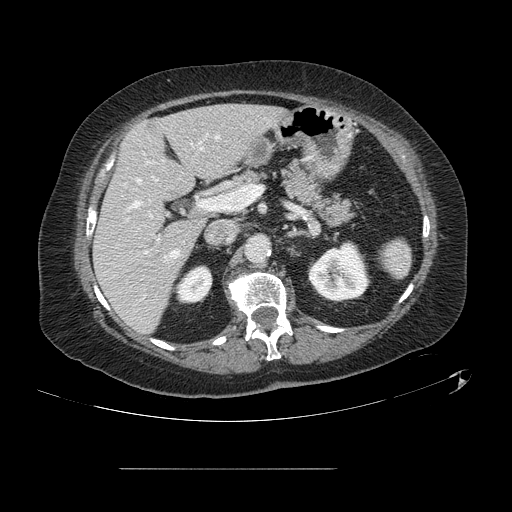
Contrast-enhanced abdominal CT, one axial slice. Position 67 of 148 along the scan axis. Intravenous contrast given. Soft-tissue window (W 400 / L 40 HU). 2.5 mm slice thickness. 512 × 512 image matrix, field of view 439 × 439 mm. Female patient, age 75 years. From the clinical record (not read from this slice): diagnosis: colorectal cancer liver metastases, imaged before liver resection; multiple liver metastases: no; largest metastasis: 2.4 cm; disease in both lobes: no.
Structures marked on this image (manually delineated by an expert):
- hepatic veins: box from (x=128, y=136) to (x=219, y=258) px
- liver: (x=94, y=105)–(x=284, y=333)
- planned liver remnant (the part of the liver to remain after resection): (x=95, y=105)–(x=284, y=333)
- portal vein (with intrahepatic branches): (x=143, y=162)–(x=209, y=254)